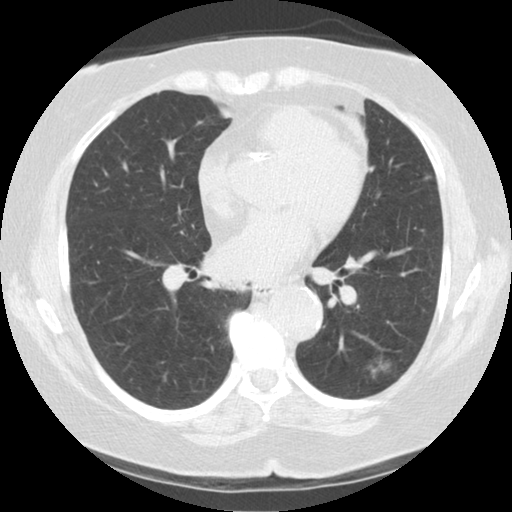
Low-dose screening chest CT, one axial slice; slice 65 of 122 in the series (ordered by position); 140 kVp; lung window (W 1500 / L -600 HU); 512 × 512 image matrix, field of view 329 × 329 mm.
Outlined on this slice (expert manual segmentation):
- lesion 1 (tumor, lower lobe of left lung): bounding box [x1, y1, x2, y2] px = [367, 357, 391, 378]